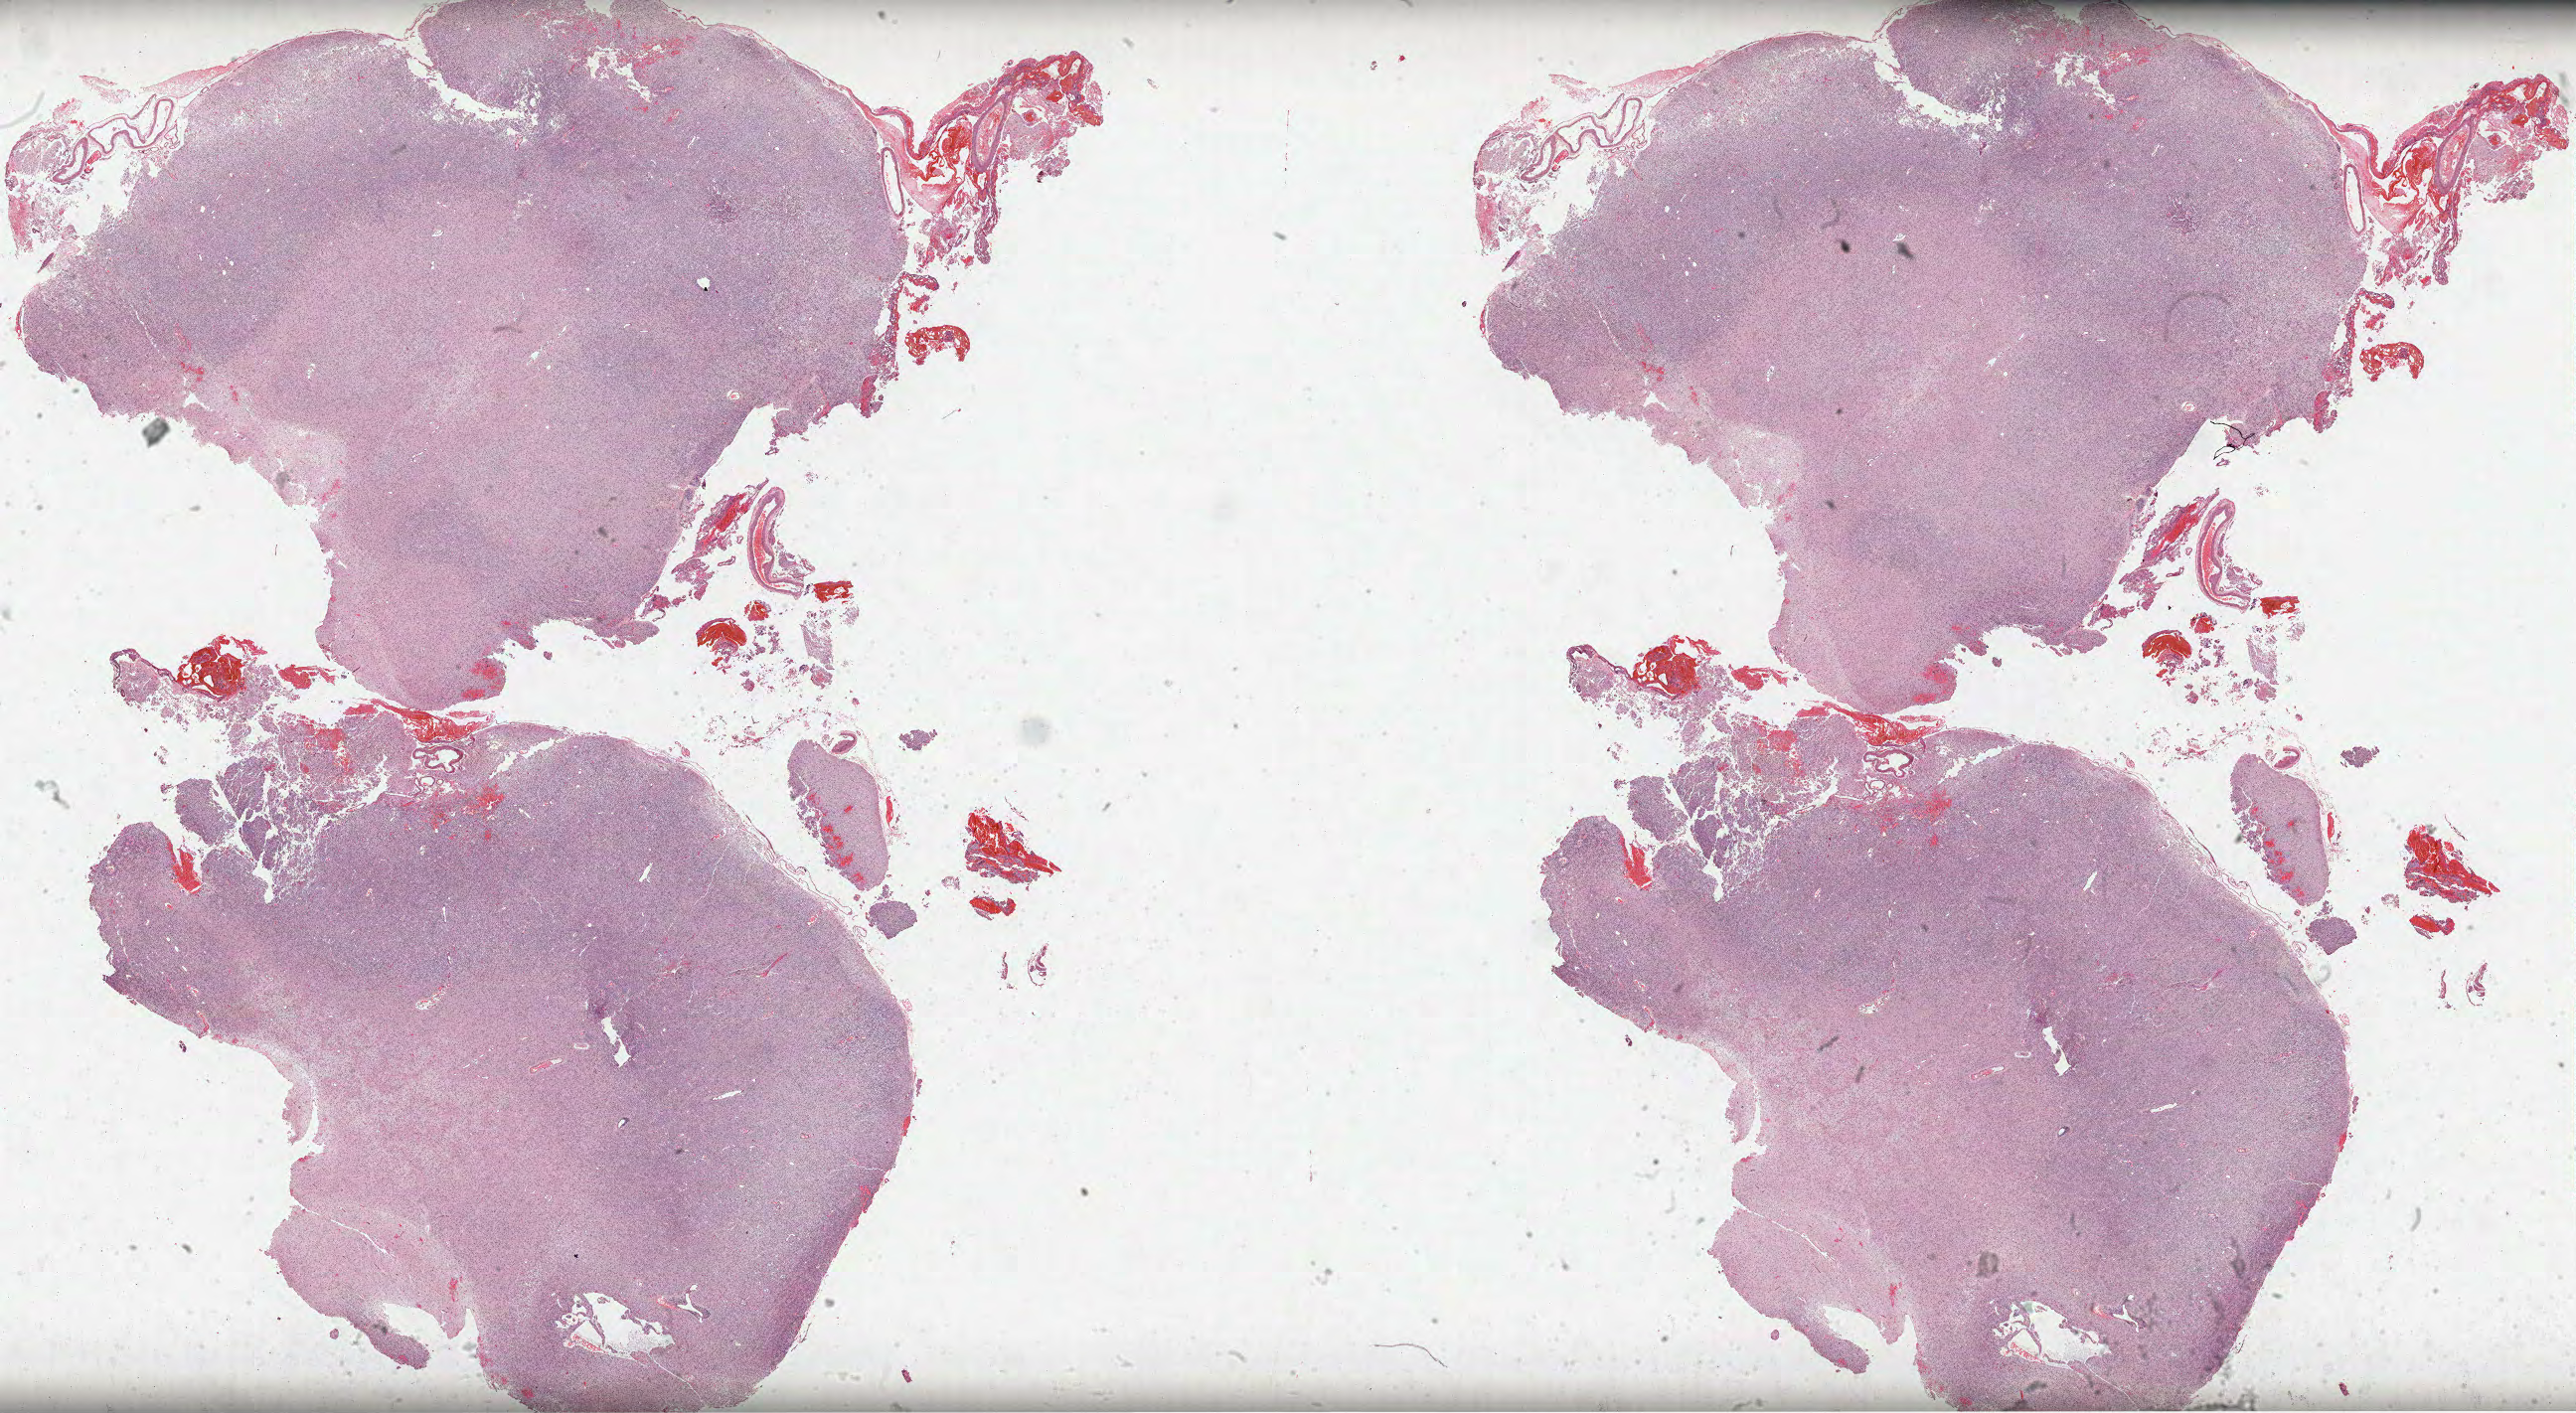
Hematoxylin and eosin (H&E) stained whole-slide image — whole scanned area (about 41.8 x 22.9 mm) shown as a low-resolution overview. Formalin-fixed paraffin-embedded (FFPE) diagnostic section. Primary tumour sample from the brain. Patient: male, age at initial diagnosis 49 years. Histologic grade: G2 (moderately differentiated).
• laterality: right
• diagnosis: Mixed glioma (cerebrum)